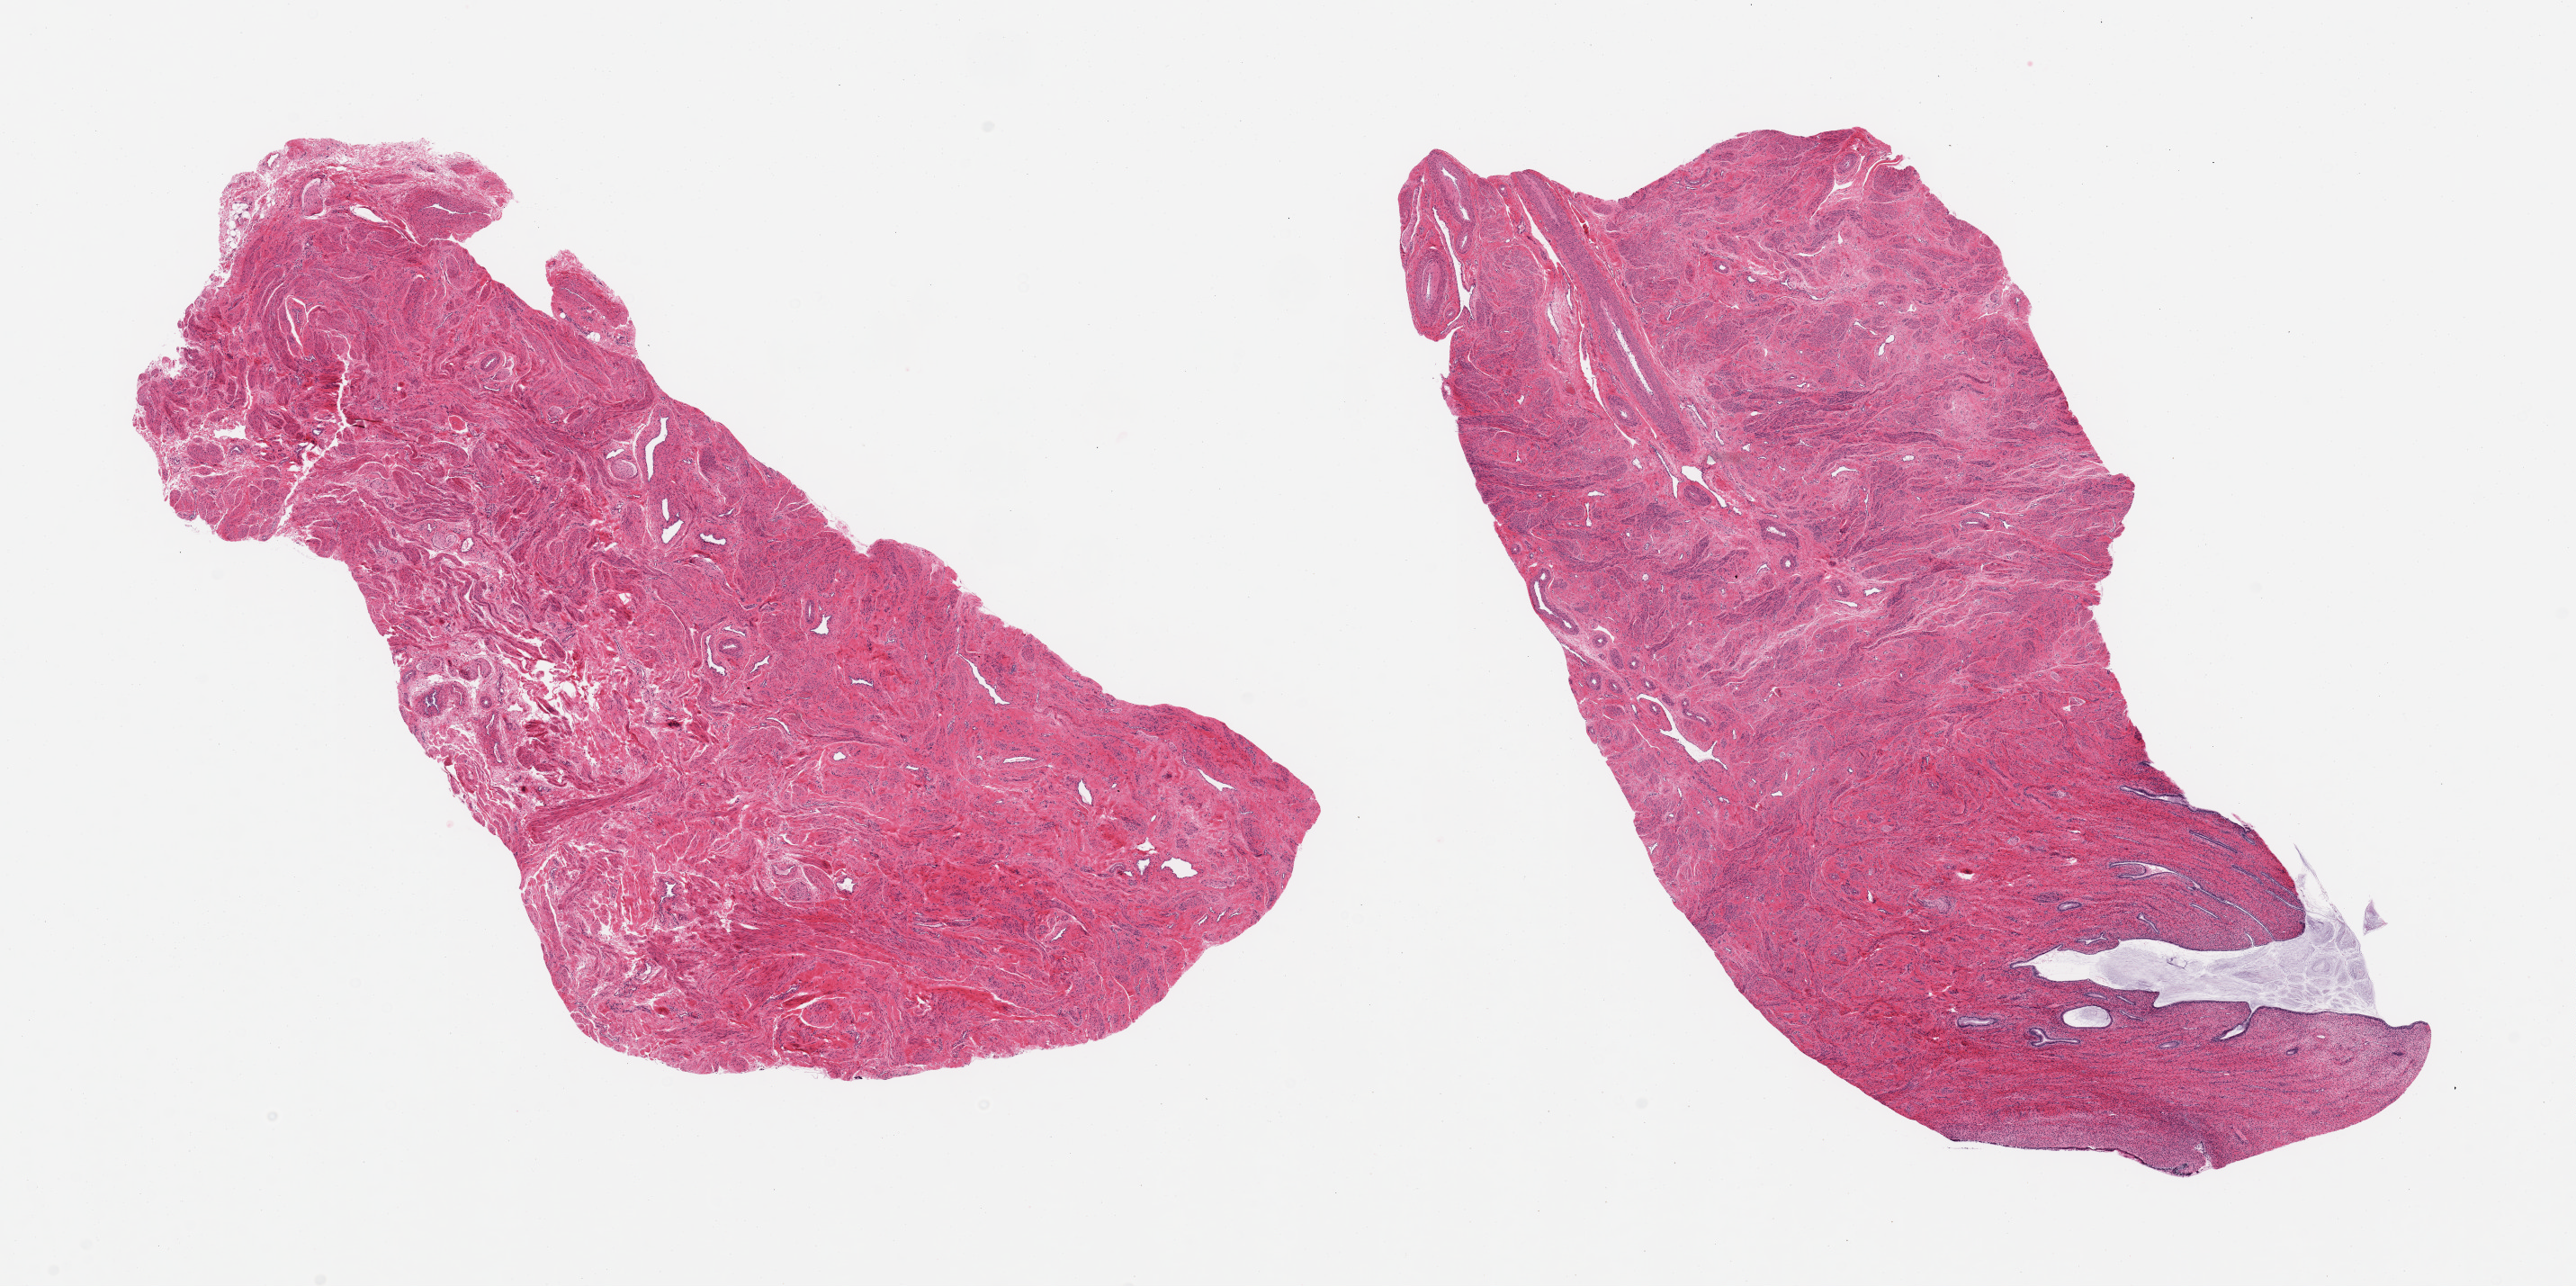
Whole-slide image, haematoxylin and eosin stain, a low-resolution overview of the entire scanned area, about 22.6 x 11.3 mm (from a 20x scan); PAXgene-fixed paraffin-embedded (PFPE) section; section of uterus (target tissue); tissue donor sample. Female donor.
* review note (as recorded): 2 pieces; no endometrium (in these cuts); 1 piece is 40% endocervix